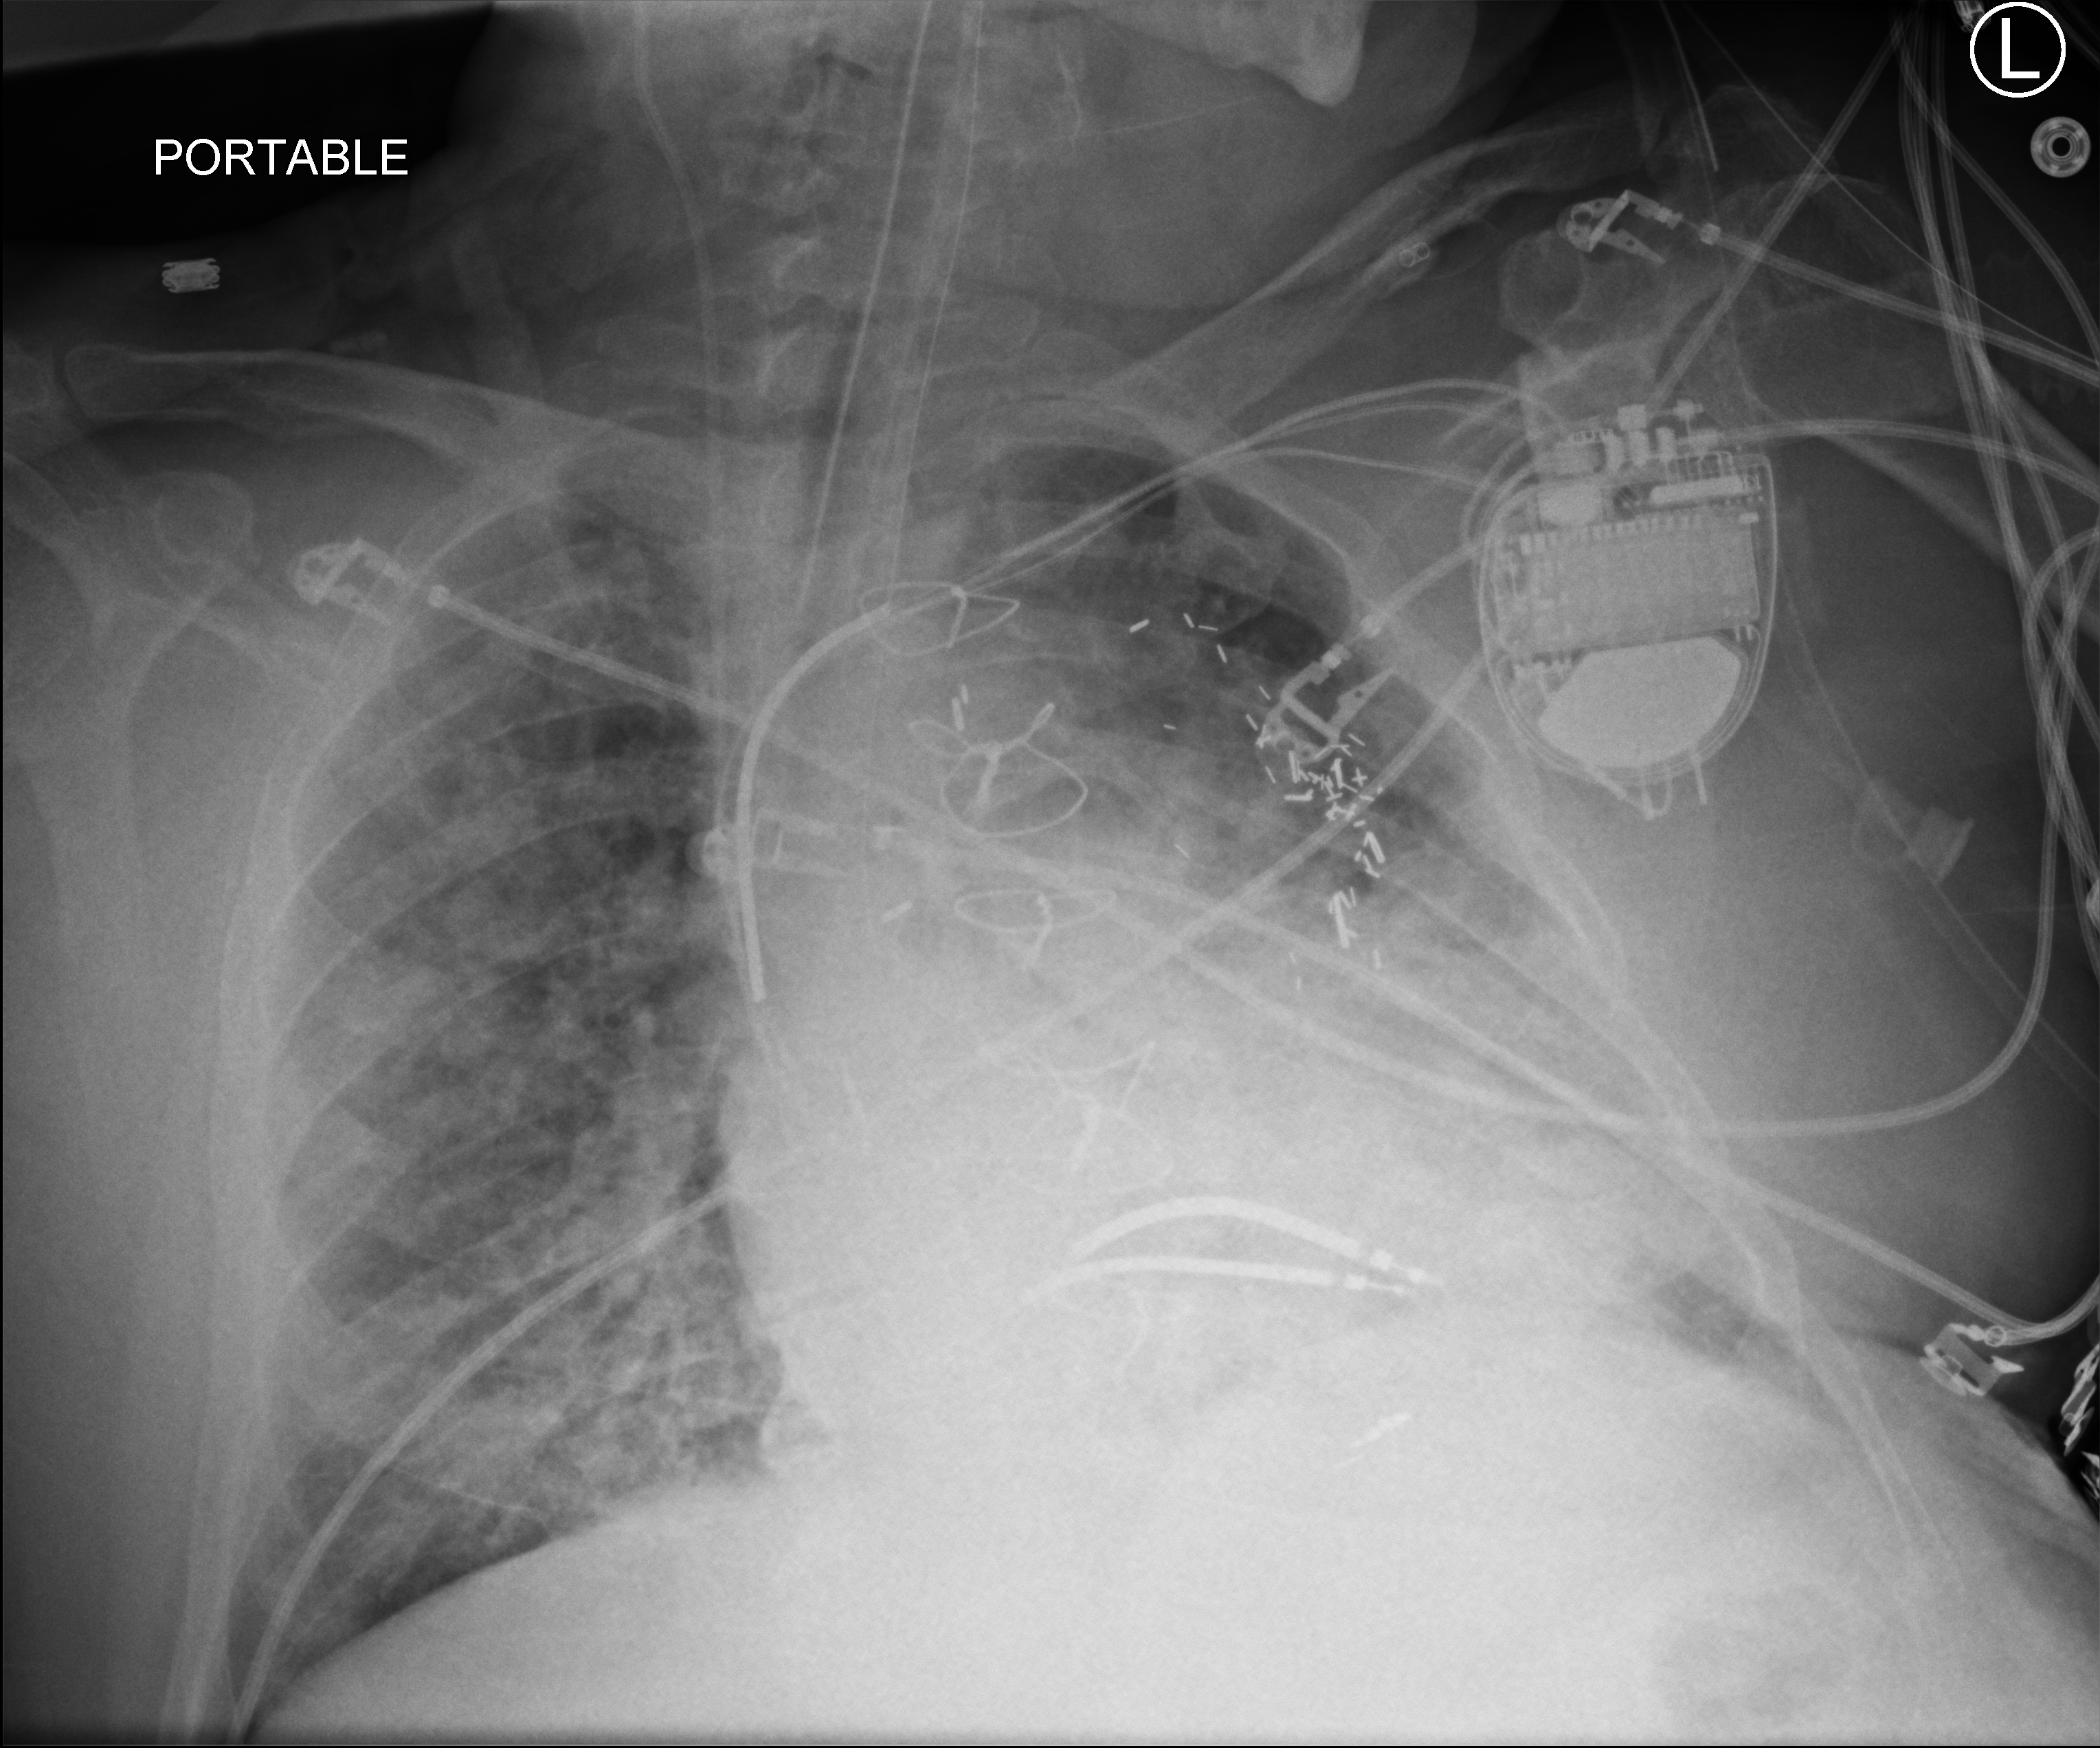
Portable chest radiograph. Male patient hospitalised with COVID-19, age 60–74 years.
Admission-level facts for this patient (not findings on this image; timing relative to this image not recorded):
- diabetes (admission record): yes
- chronic kidney disease (admission record): no
- other chronic lung disease (admission record): no